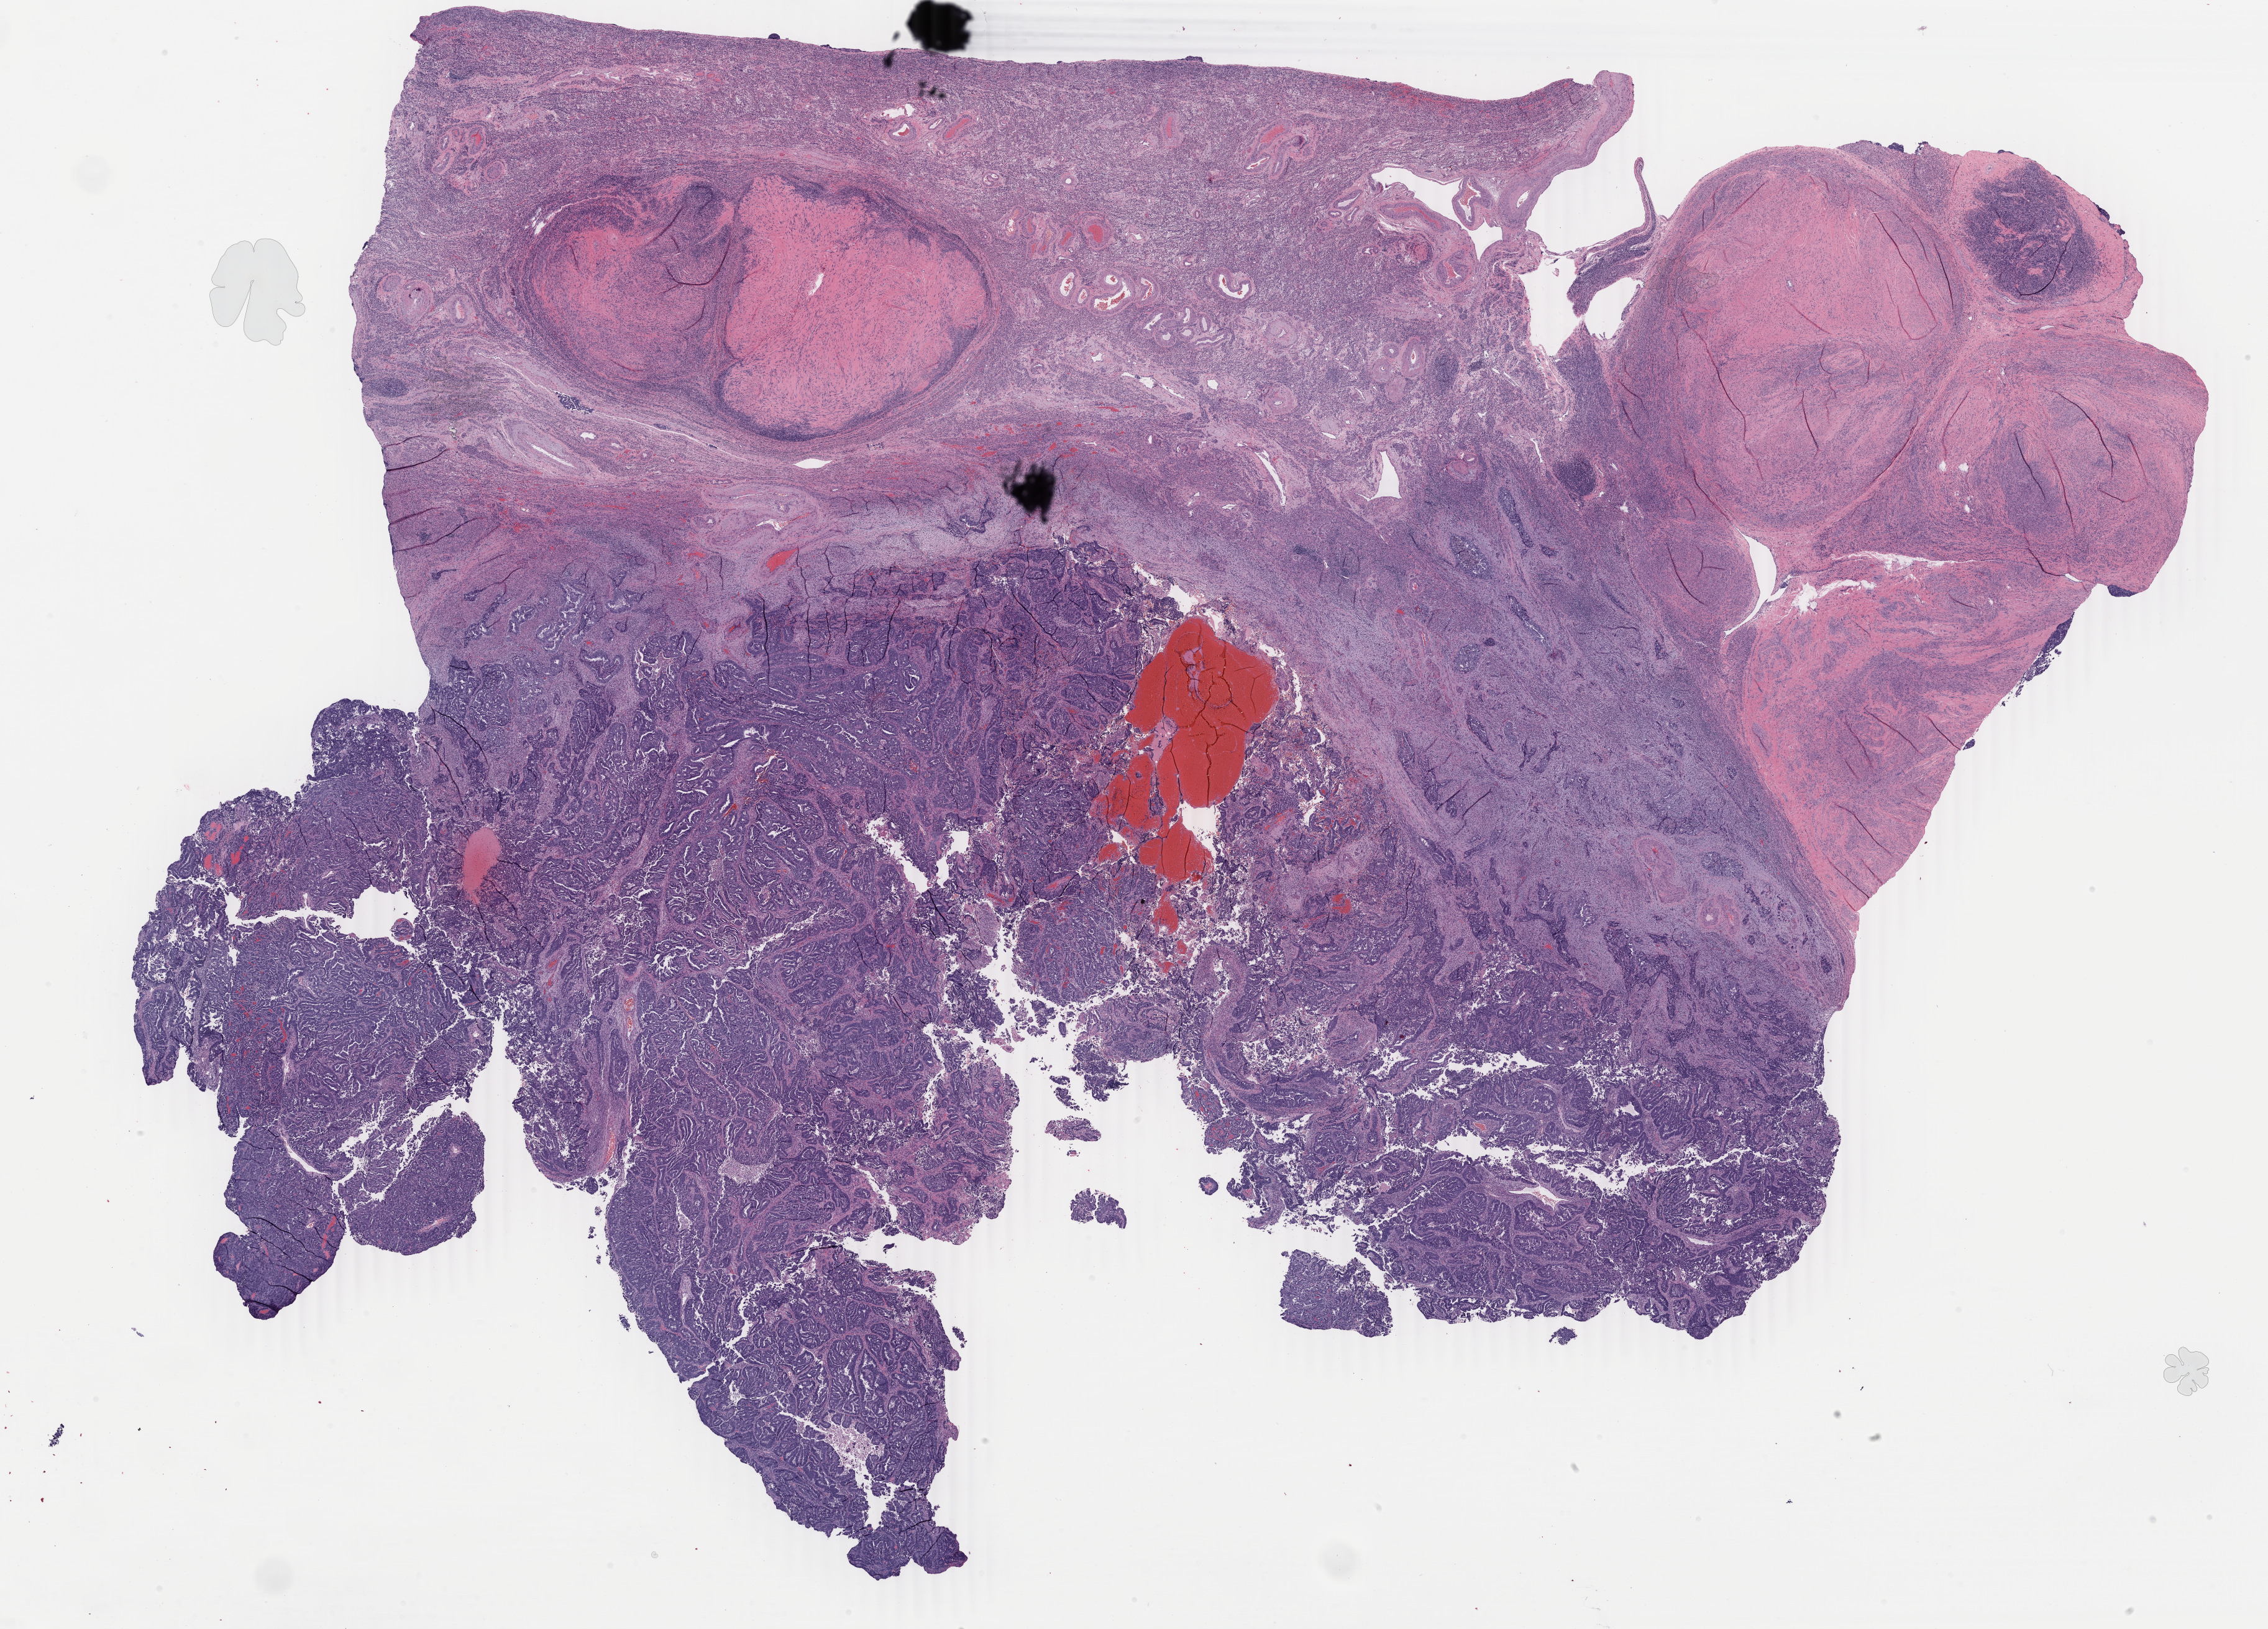
Digitized Hematoxylin and eosin (H&E) stained tissue section (whole slide) — shown as a low-resolution overview of the whole scanned area (about 29.0 x 20.8 mm). Formalin-fixed paraffin-embedded (FFPE) diagnostic section. Uterus, primary tumour sample. Female, age 67 years at initial diagnosis. Histologic grade: G3 (poorly differentiated).
* FIGO stage: IIIA
* pathologic diagnosis: Serous cystadenocarcinoma, NOS (endometrium)